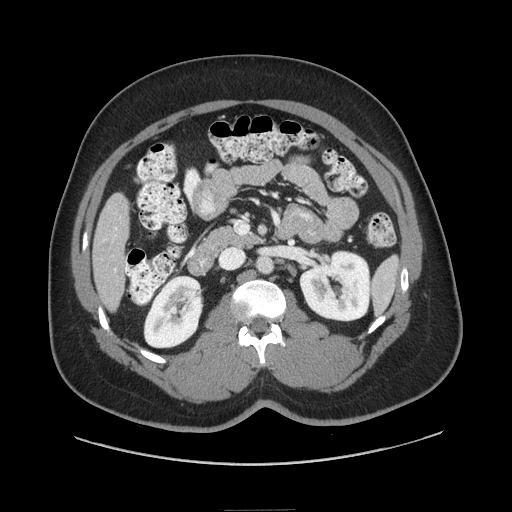
Contrast-enhanced abdominal CT (liver protocol), one axial slice; slice 23 of 87 in the series (ordered by position); reconstruction kernel STANDARD; 140 kVp; soft-tissue window (W 400 / L 40 HU); 512 × 512 image matrix, field of view 440 × 440 mm. Case-level facts recorded for this patient, not image findings: diagnosis: hepatocellular carcinoma (patient treated with transarterial chemoembolisation; whether this scan precedes or follows treatment is not stated here); TNM stage (as recorded): Stage-II; Child-Pugh class: A; tumour differentiation: moderately differentiated; tumour nodularity: uninodular.
Annotated regions visible in this slice (semi-automatic segmentation, software-assisted and operator-edited):
- liver parenchyma outside the tumour (the mass and vessels are separate outlines, so this box may not span the whole liver): bounding box [x1, y1, x2, y2] px = [92, 192, 128, 310]
- liver vessels: [114, 228, 117, 271]